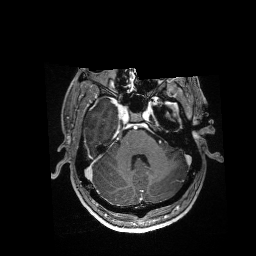
Brain MRI from a brain-tumour surgery series, one axial slice; position 118 of 176 along the scan axis; T1-weighted post-contrast; 1 mm slice thickness; 256 × 256 image matrix. From the clinical record (not read from this slice): histopathology: Glioblastoma; WHO grade: 4; IDH mutation: no; tumour location: Left Anterior/Superior Temporal.
Outlined on this slice (expert manual segmentation):
- residual tumour: box from (x=167, y=103) to (x=178, y=111) px